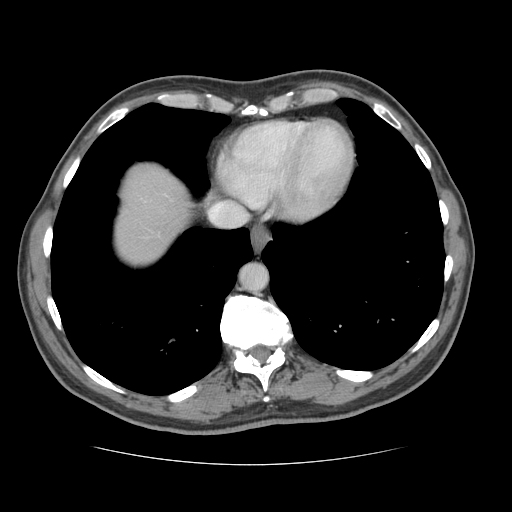
Contrast-enhanced abdominal CT, one axial slice. 120 kVp. Intravenous contrast given. Soft-tissue window (W 400 / L 40 HU). 2.5 mm slice thickness. 512 × 512 image matrix. Male patient, age 68 years. From the clinical record (not read from this slice): diagnosis: colorectal cancer liver metastases, imaged before liver resection; multiple liver metastases: yes; largest metastasis: 2.2 cm; disease in both lobes: no.
Outlined on this slice (manually delineated by an expert):
- hepatic veins: bounding box [x1, y1, x2, y2] px = [227, 204, 242, 214]
- liver: [117, 170, 179, 253]
- planned liver remnant (the part of the liver to remain after resection): [117, 170, 179, 252]